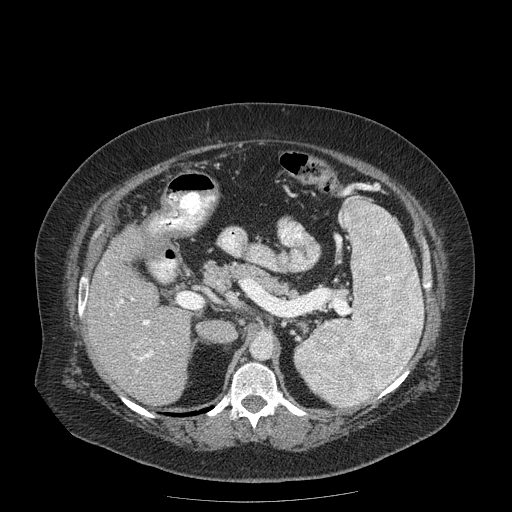
Contrast-enhanced abdominal CT (liver protocol), one axial slice. Position 95 of 204 along the scan axis. Reconstruction kernel STANDARD. Soft-tissue window (W 400 / L 40 HU). 512 × 512 image matrix, field of view 440 × 440 mm. From the clinical record (not read from this slice): diagnosis: hepatocellular carcinoma (patient treated with transarterial chemoembolisation; whether this scan precedes or follows treatment is not stated here); TNM stage (as recorded): Stage-IIIB; Child-Pugh class: A; tumour nodularity: uninodular.
Annotated regions visible in this slice (semi-automatically segmented with operator editing):
- liver parenchyma outside the tumour (the mass and vessels are separate outlines, so this box may not span the whole liver): bounding box <86,226,192,406> (left, top, right, bottom; pixels)
- liver vessels: <106,272,164,372>